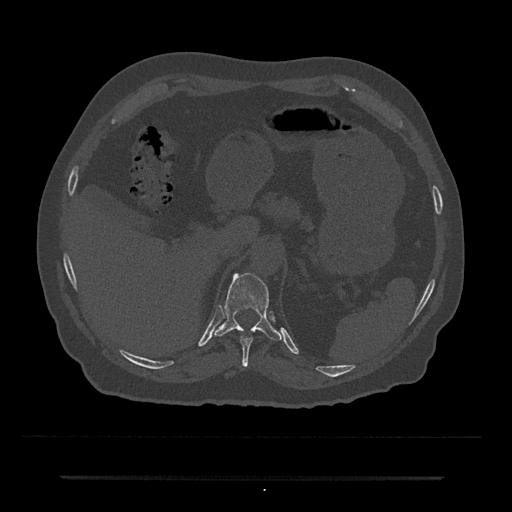
CT including the spine, one axial slice; slice 193 of 797 in the series (ordered by position); reconstruction kernel Br40s/3; 120 kVp; bone window (W 1800 / L 400 HU); 512 × 512 image matrix, field of view 437 × 437 mm. Patient: male, 69 years. Case-level facts recorded for this patient, not image findings: primary cancer: prostate.
Annotated regions visible in this slice (semi-automatic segmentation, software-assisted and operator-edited):
- T10 vertebra: bounding box [x1, y1, x2, y2] px = [240, 336, 253, 366]
- T11 vertebra: [214, 273, 283, 341]